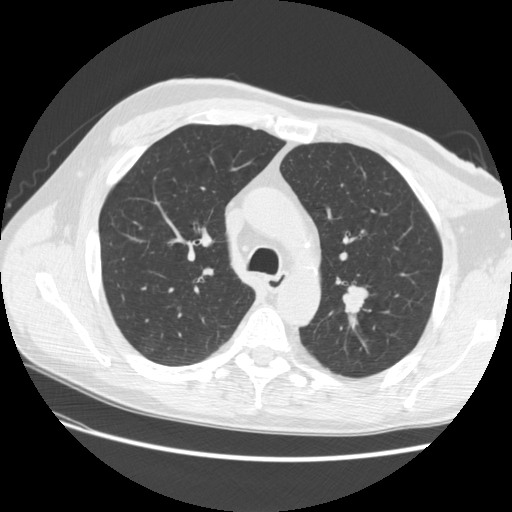
Low-dose screening chest CT, one axial slice; position 181 of 256 along the scan axis; reconstruction kernel STANDARD; 120 kVp; lung window (W 1500 / L -600 HU); 512 × 512 image matrix, field of view 366 × 366 mm.
Annotated regions visible in this slice (expert manual segmentation):
- lesion 1 (tumor, upper lobe of left lung): bounding box <343,288,367,313> (left, top, right, bottom; pixels)